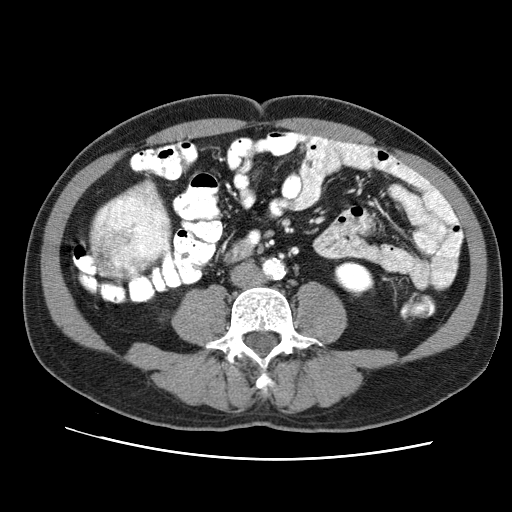
Contrast-enhanced abdominal CT (liver protocol), one axial slice. Position 8 of 71 along the scan axis. Reconstruction kernel STANDARD. 120 kVp. Soft-tissue window (W 400 / L 40 HU). 512 × 512 image matrix, field of view 360 × 360 mm. Case-level facts recorded for this patient, not image findings: diagnosis: hepatocellular carcinoma (patient treated with transarterial chemoembolisation; whether this scan precedes or follows treatment is not stated here); TNM stage (as recorded): Stage-II; Child-Pugh class: A; tumour nodularity: multinodular.
Outlined on this slice (semi-automatically segmented with operator editing):
- mass: bounding box [x1, y1, x2, y2] px = [89, 188, 168, 275]